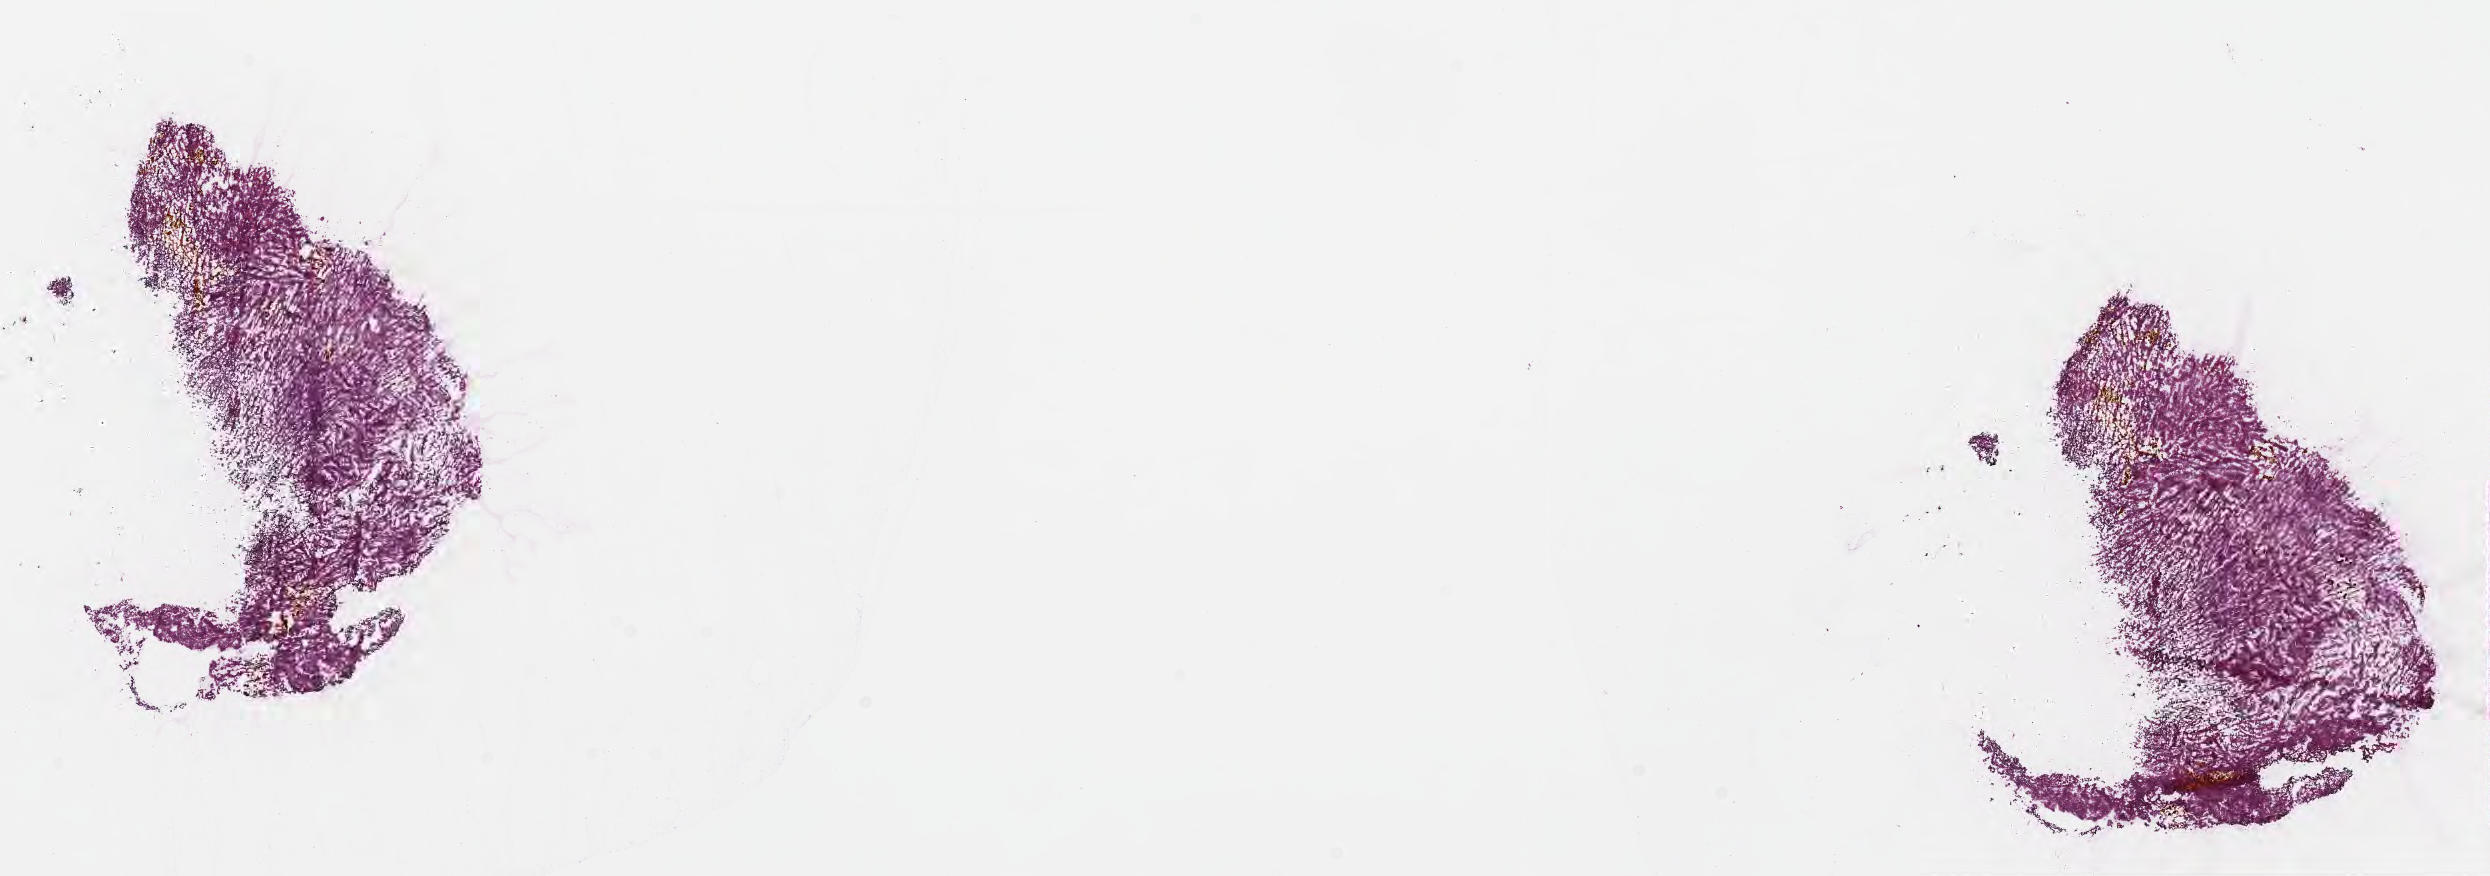
Digitized haematoxylin and eosin-stained section — whole scanned area (about 20.1 x 7.1 mm) shown as a low-resolution overview. Frozen section (tissue freezing medium). Premalignant lesion from a patient with noninfiltrating intraductal papillary adenocarcinoma. Site: gallbladder. Male patient; age at initial diagnosis 65 years. Composition of this section per pathologist review: tumor cells 90%, tumor nuclei 90%, stromal cells 10%, necrosis 0%, normal cells 0%. Inflammatory infiltration, as recorded: lymphocyte infiltration 2%, monocyte infiltration 1%, neutrophil infiltration 3%.
This section: sample classed premalignant; the patient's recorded diagnosis is given above. Section: top of the tissue portion.